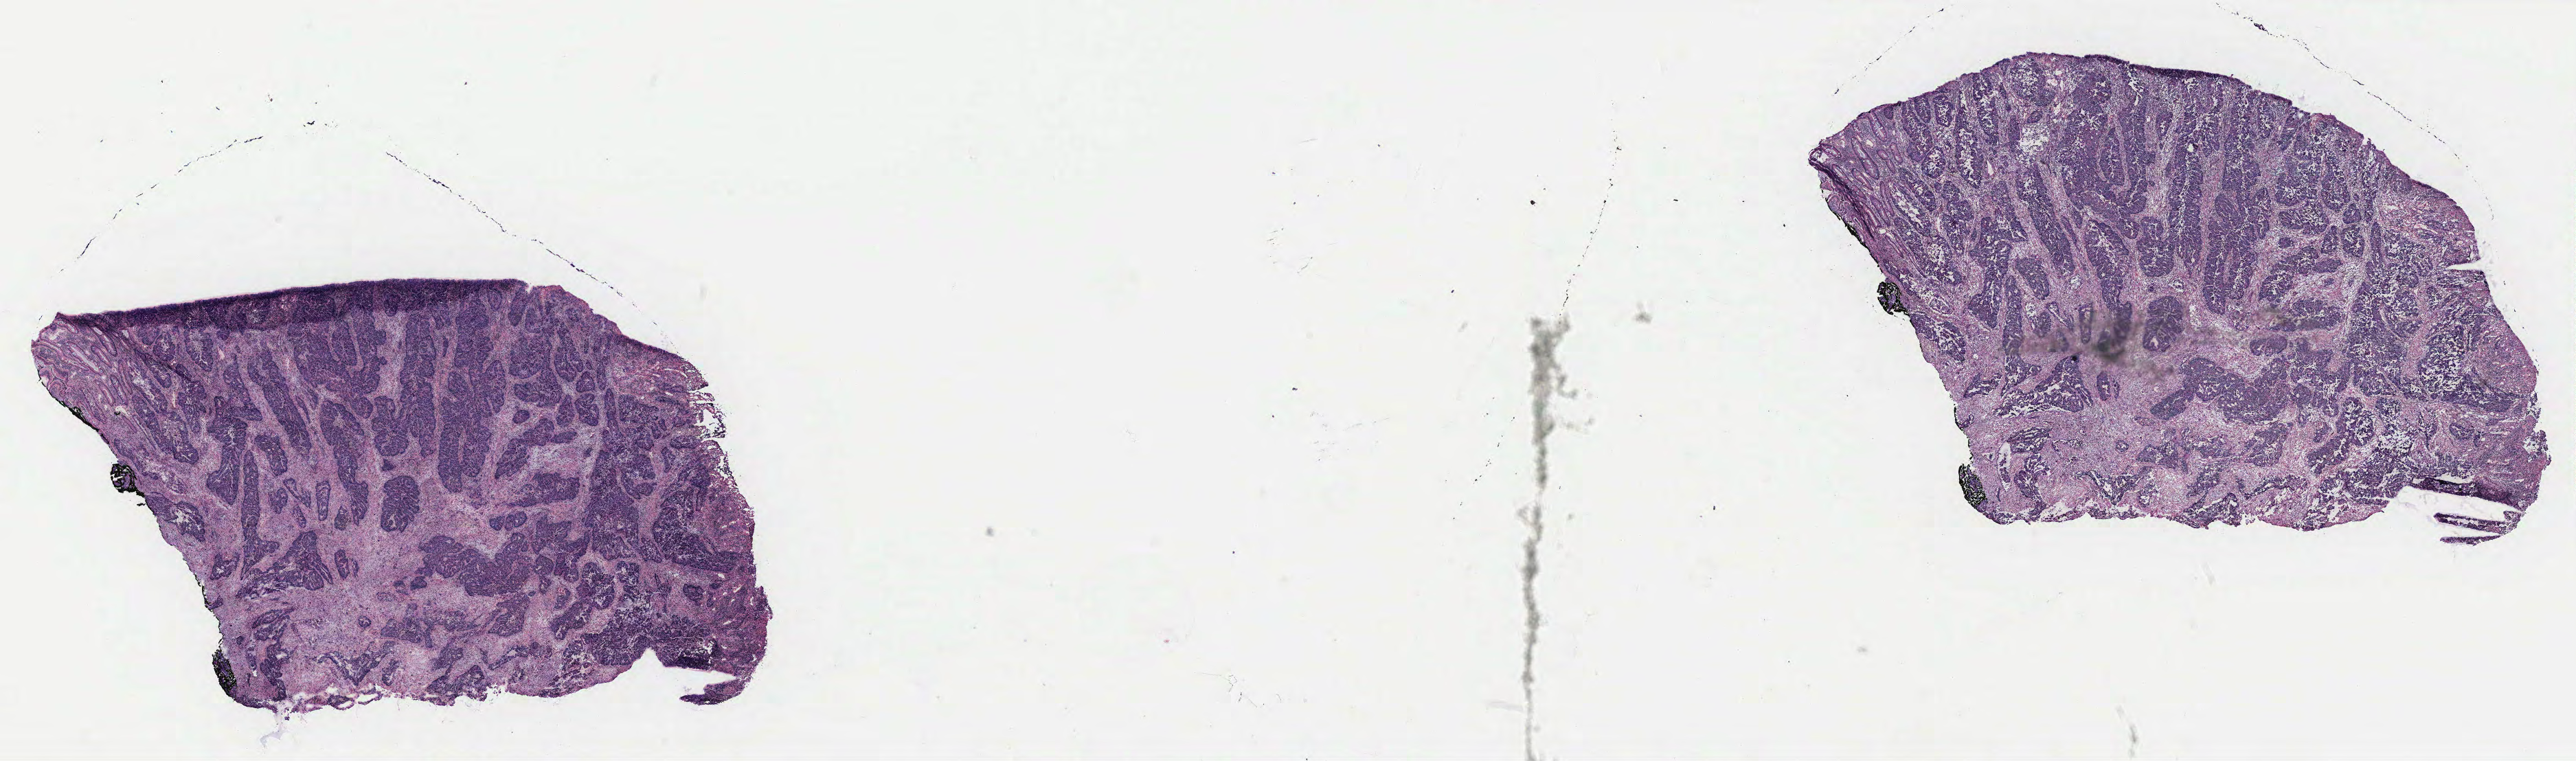
Digitized Hematoxylin and eosin (H&E) stained tissue section (whole slide) — low-resolution overview of the scanned area, about 30.0 x 8.9 mm (from a 40x scan); colon, tissue type not recorded. Patient sex: female.
Patient diagnosis: Adenocarcinoma, NOS (rectum, NOS).